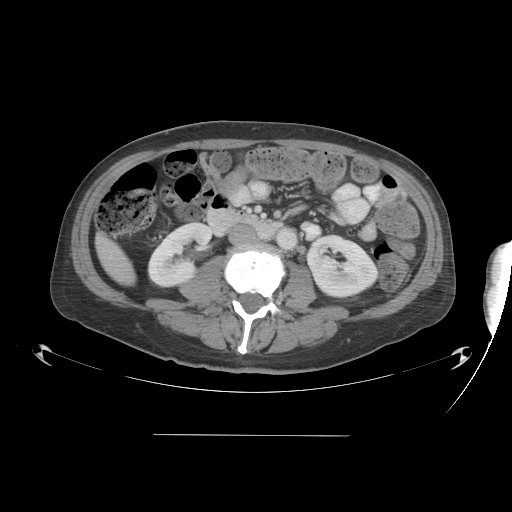
Contrast-enhanced abdominal CT, one axial slice; slice 10 of 48 in the series (ordered by position); reconstruction kernel STANDARD; 120 kVp; intravenous contrast given; soft-tissue window (W 400 / L 40 HU); 512 × 512 image matrix, field of view 486 × 486 mm. Male patient, age 65 years. From the clinical record (not read from this slice): diagnosis: colorectal cancer liver metastases, imaged before liver resection; multiple liver metastases: yes; largest metastasis: 11 cm; disease in both lobes: yes.
Structures marked on this image (outlined manually by an expert reader):
- liver: box from (x=98, y=237) to (x=134, y=283) px